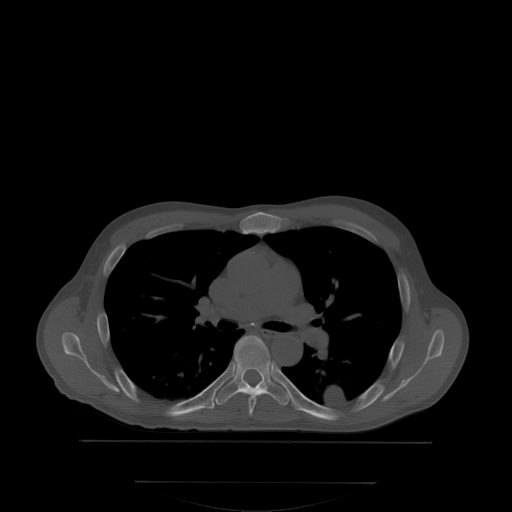
CT including the spine, one axial slice; position 240 of 350 along the scan axis; bone window (W 1800 / L 400 HU); 512 × 512 image matrix, field of view 500 × 500 mm. Patient: male, 58 years. From the clinical record (not read from this slice): primary cancer: prostate.
Outlined on this slice (semi-automatically segmented with operator editing):
- T5 vertebra: bounding box (x1, y1, x2, y2) in pixels: (249, 397, 256, 413)
- T6 vertebra: (203, 335, 291, 404)